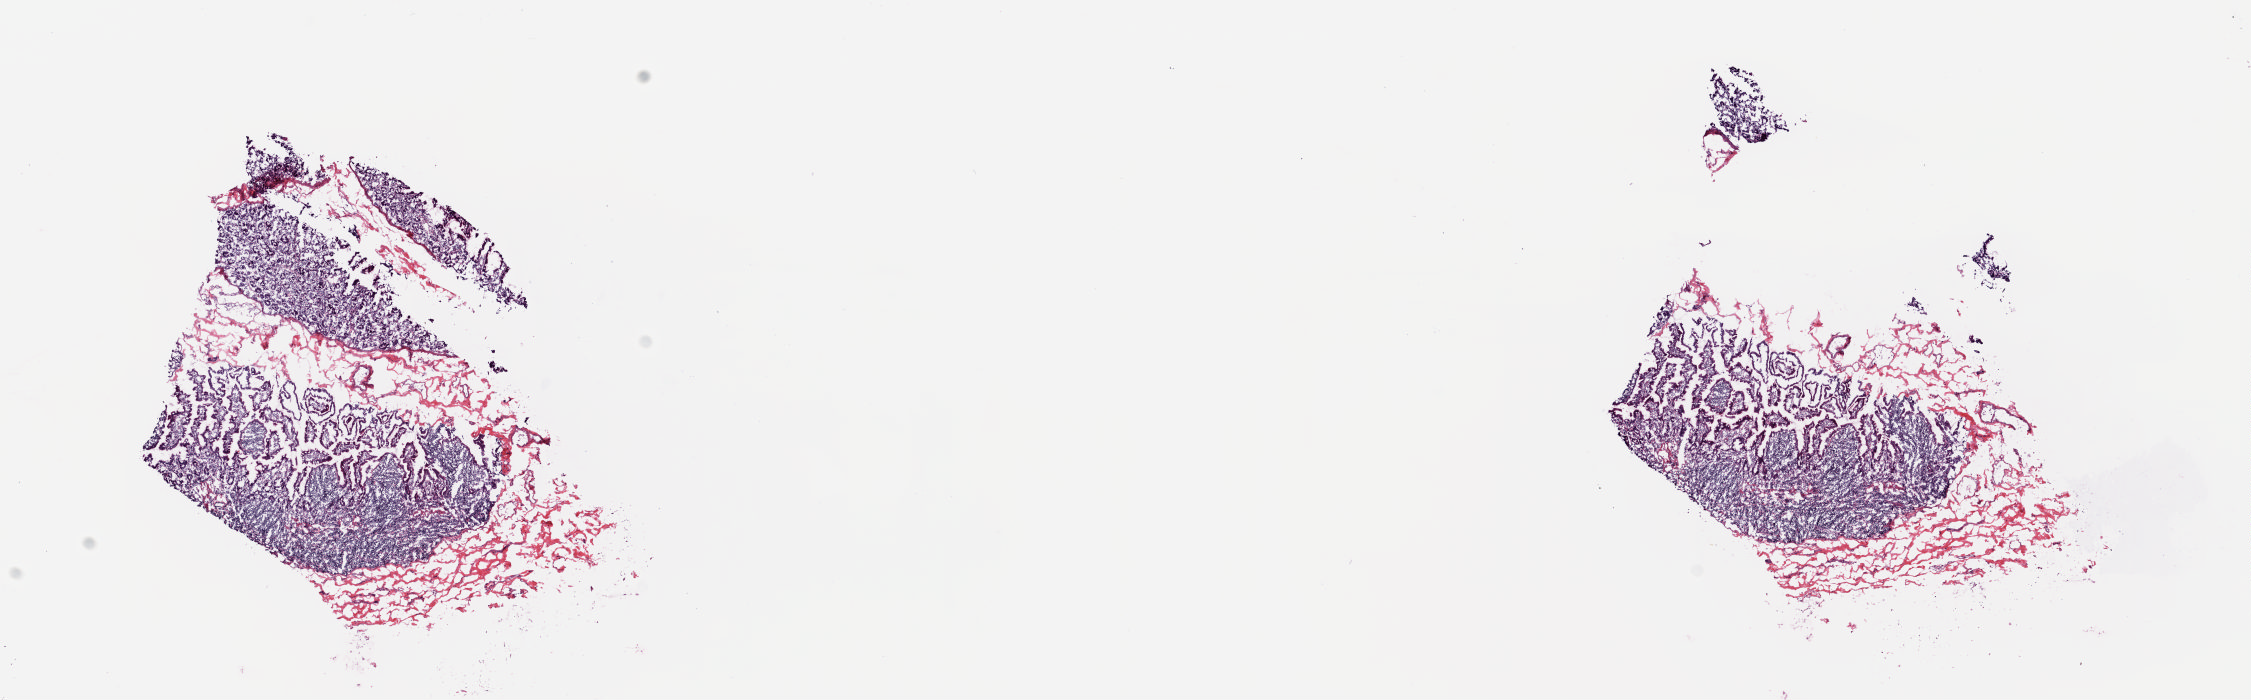
Digitized H&E tissue section (whole slide) — a low-resolution overview of the entire scanned area, about 17.9 x 5.6 mm, frozen section from the top of the tissue portion, sample: solid tissue normal (non-tumour tissue), pancreas. Female patient; age at initial diagnosis 54 years.
This section: solid tissue normal sample (biorepository sample class). Patient diagnosis: Infiltrating duct carcinoma, NOS (head of pancreas).